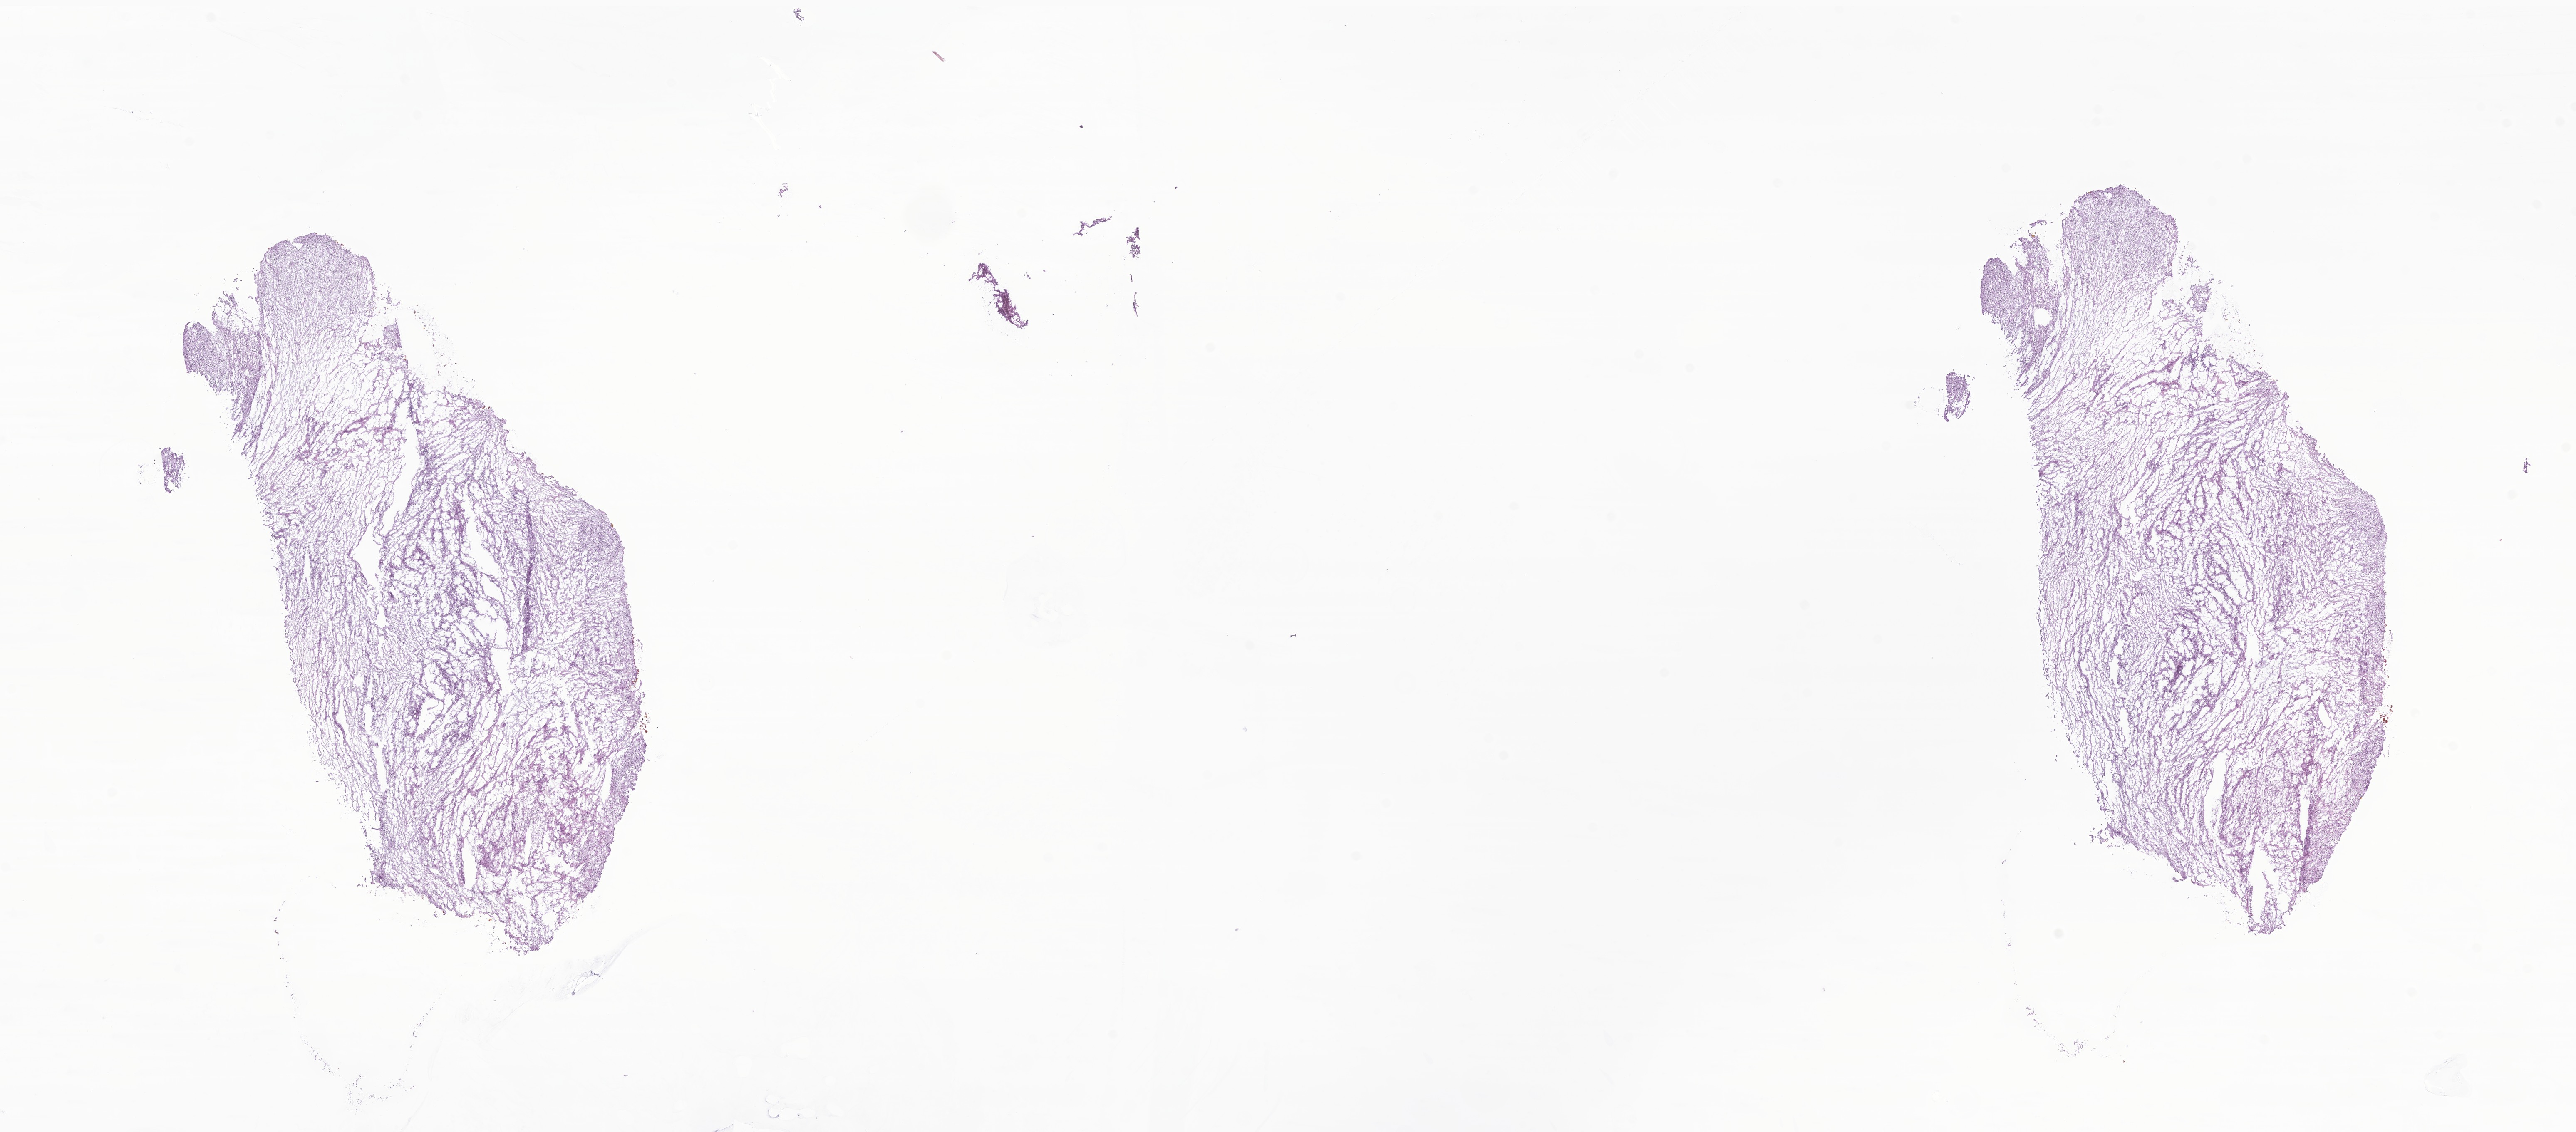
Digitized hematoxylin and eosin (H&E)-stained section of tumor tissue from the soft tissue of lower extremity, shown as a low-resolution overview of the whole scanned area (about 26.1 x 11.5 mm); frozen section (OCT-embedded). Patient: female, age 167 months (13 years 11 months).
• diagnosis: Angiomatoid fibrous histiocytoma